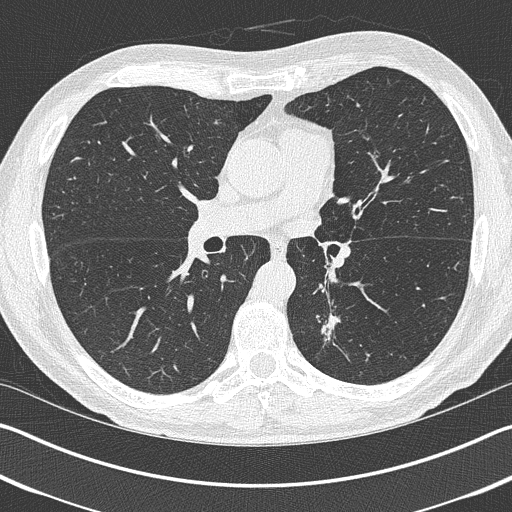
Low-dose screening chest CT, one axial slice; reconstruction kernel B50f; 120 kVp; lung window (W 1500 / L -600 HU); 1 mm slice thickness; 512 × 512 image matrix.
Annotated regions visible in this slice (expert manual segmentation):
- lesion 1 (tumor, lower lobe of left lung): bounding box (x1, y1, x2, y2) in pixels: (321, 313, 340, 342)